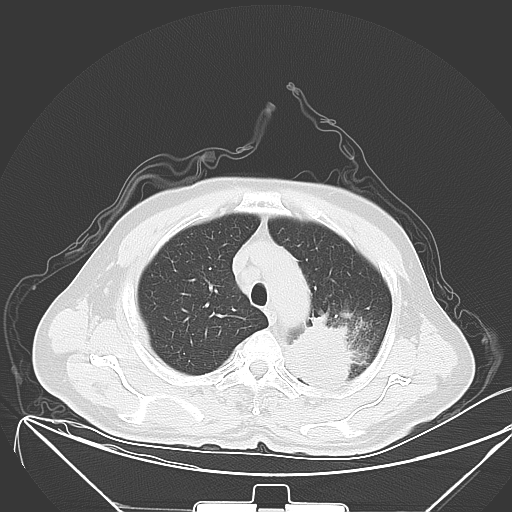
Chest CT, one axial slice. Slice 47 of 64 in the series (ordered by position). 120 kVp. Lung window (W 1500 / L -600 HU). 512 × 512 image matrix, field of view 431 × 431 mm. Male patient, age 58 years. Case-level facts recorded for this patient, not image findings: clinical TNM (as recorded): T2b N3 M1b.
Structures marked on this image (bounding box drawn by a radiologist):
- lung tumour (recorded histology: adenocarcinoma): bounding box [x1, y1, x2, y2] px = [281, 307, 357, 394]